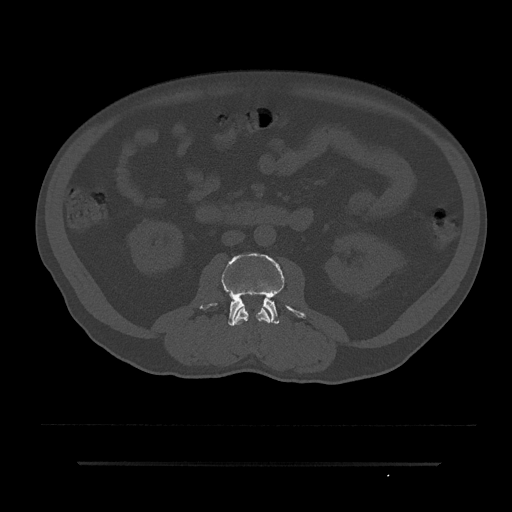
CT including the spine, one axial slice; position 29 of 797 along the scan axis; 120 kVp; bone window (W 1800 / L 400 HU); 0.5 mm slice thickness; 512 × 512 image matrix, field of view 464 × 464 mm. Patient: male, 59 years. From the clinical record (not read from this slice): primary cancer: bile ducts; vertebrae with lytic lesions (as recorded): T10.
Annotated regions visible in this slice (semi-automatic segmentation, software-assisted and operator-edited):
- L2 vertebra: bounding box [x1, y1, x2, y2] px = [233, 304, 273, 325]
- L3 vertebra: [200, 253, 306, 326]